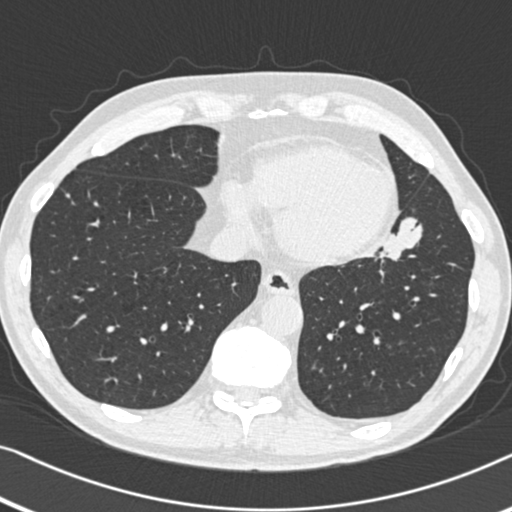
Low-dose screening chest CT, one axial slice. Slice 136 of 383 in the series (ordered by position). Reconstruction kernel B30f. Lung window (W 1500 / L -600 HU). 512 × 512 image matrix.
Outlined on this slice (manually delineated by an expert):
- lesion 1 (tumor, upper lobe of left lung): bounding box [x1, y1, x2, y2] px = [380, 217, 423, 261]